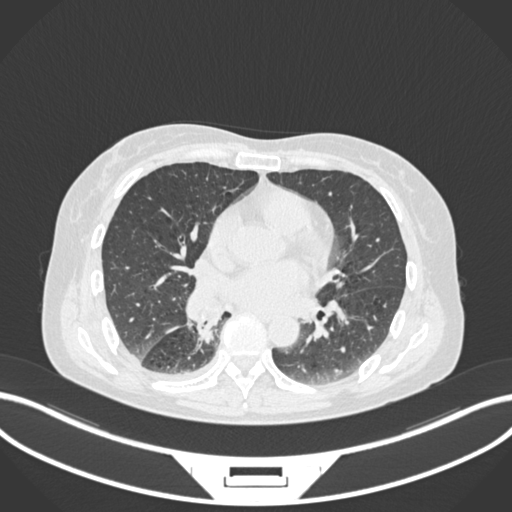
Chest CT, one axial slice. Position 79 of 168 along the scan axis. 120 kVp. Lung window (W 1500 / L -600 HU). 1 mm slice thickness. 512 × 512 image matrix, field of view 400 × 400 mm. Patient: female, 63 years. From the clinical record (not read from this slice): clinical TNM (as recorded): T1c N0 M0.
Annotated regions visible in this slice (rectangle marked by the reading radiologist):
- lung tumour (recorded histology: adenocarcinoma): bounding box <190,297,224,346> (left, top, right, bottom; pixels)